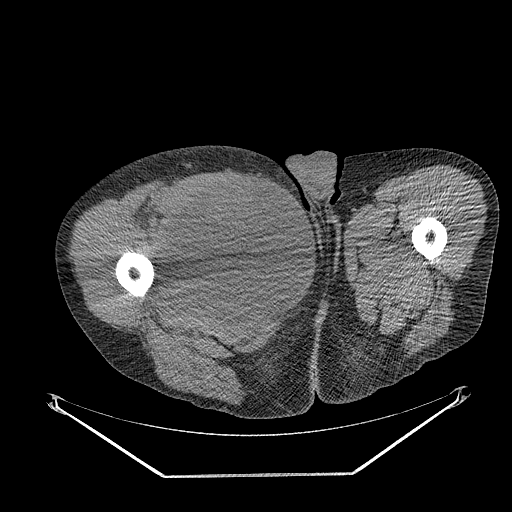
CT of an extremity soft-tissue mass (from a PET/CT study), one axial slice; slice 274 of 311 in the series (ordered by position); reconstruction kernel STANDARD; soft-tissue window (W 400 / L 40 HU); 3.75 mm slice thickness; 512 × 512 image matrix, field of view 500 × 500 mm. Male patient. From the clinical record (not read from this slice): histological type: undifferentiated - pleiomorphic; grade: high; site of the primary tumour: right thigh.
Outlined on this slice (expert contour drawn on MRI and transferred to this co-registered scan by the dataset authors):
- gross tumour volume including surrounding oedema: bounding box <162,176,266,280> (left, top, right, bottom; pixels)
- gross tumour volume (mass): <162,176,266,280>